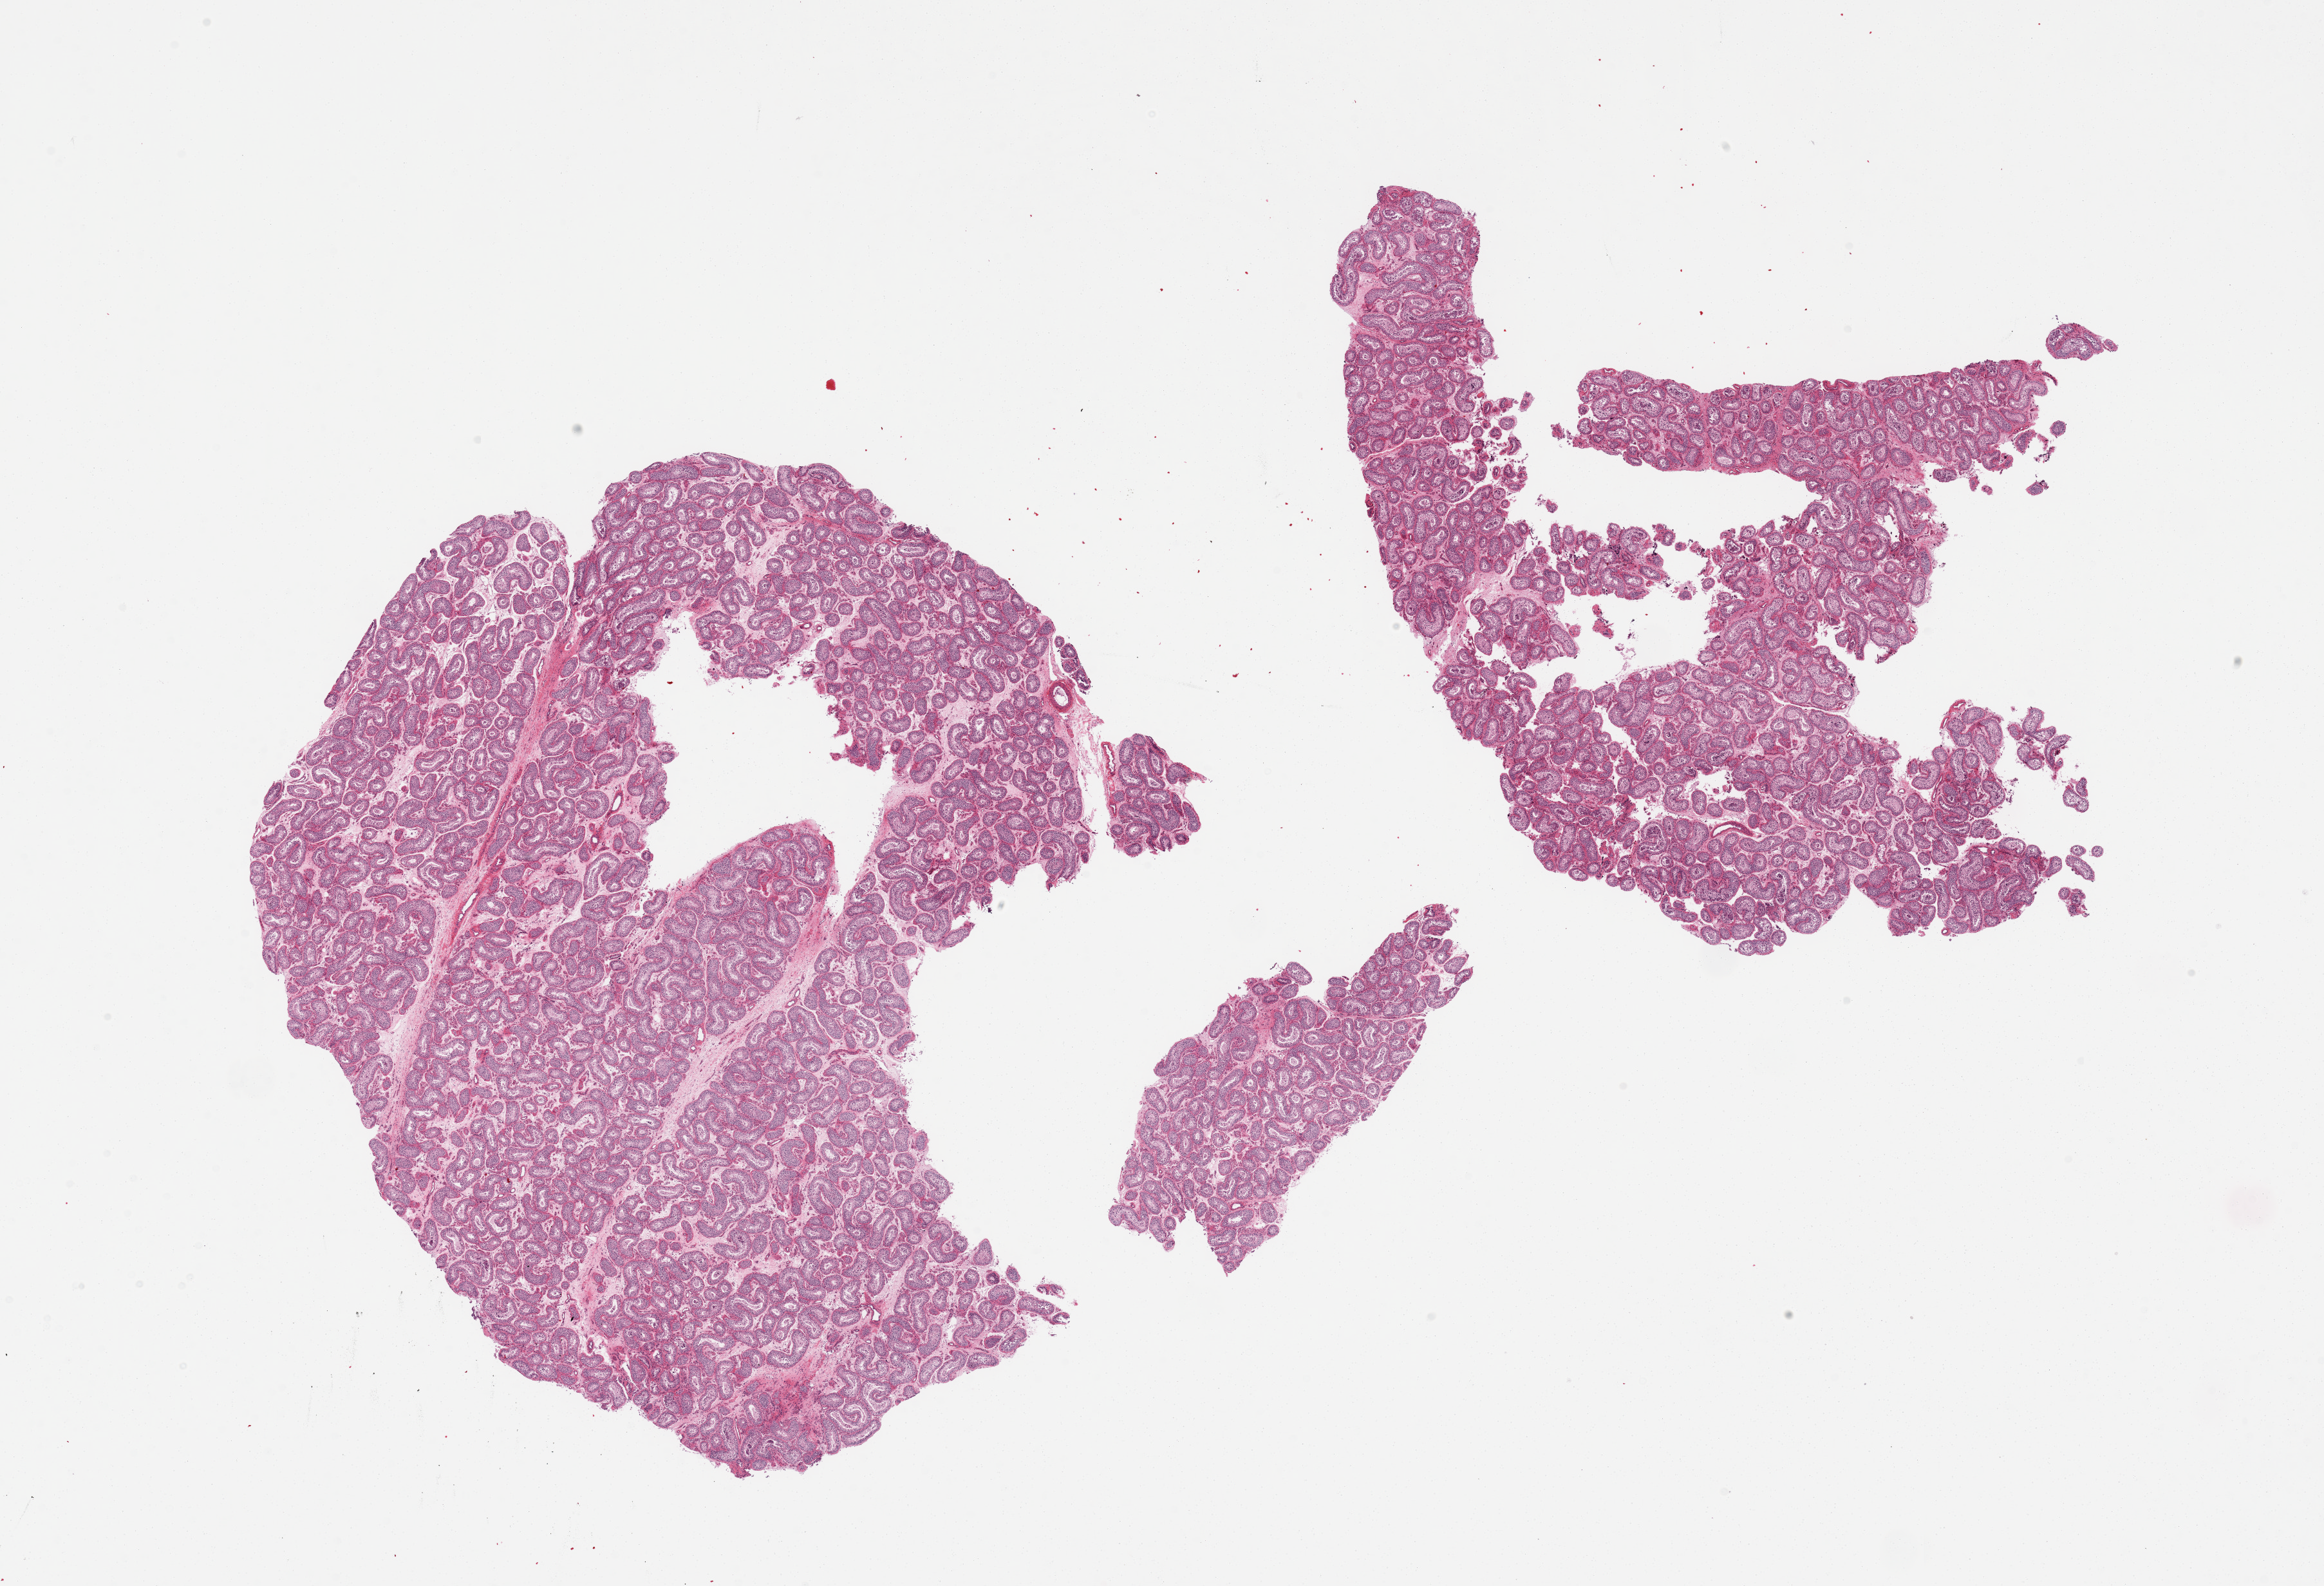
Digitized hematoxylin and eosin (H&E)-stained section — whole scanned area (about 28.5 x 19.5 mm, from a 20x scan) shown as a low-resolution overview, PAXgene-fixed paraffin-embedded (PFPE) section, section of testis (target tissue), donor tissue sample. Donor sex: male.
Reviewer comment on this tissue sample: 3 pieces, active spermatogenesis.